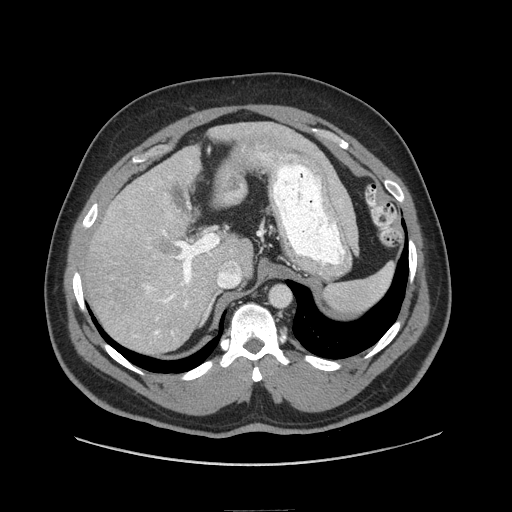
Contrast-enhanced abdominal CT (liver protocol), one axial slice; position 52 of 87 along the scan axis; reconstruction kernel STANDARD; 140 kVp; soft-tissue window (W 400 / L 40 HU); 512 × 512 image matrix. Case-level facts recorded for this patient, not image findings: diagnosis: hepatocellular carcinoma (patient treated with transarterial chemoembolisation; whether this scan precedes or follows treatment is not stated here); TNM stage (as recorded): Stage-II.
Outlined on this slice (semi-automatically segmented with operator editing):
- liver parenchyma outside the tumour (the mass and vessels are separate outlines, so this box may not span the whole liver): bounding box (x1, y1, x2, y2) in pixels: (84, 124, 320, 352)
- mass: (148, 228, 180, 267)
- liver vessels: (134, 154, 265, 337)